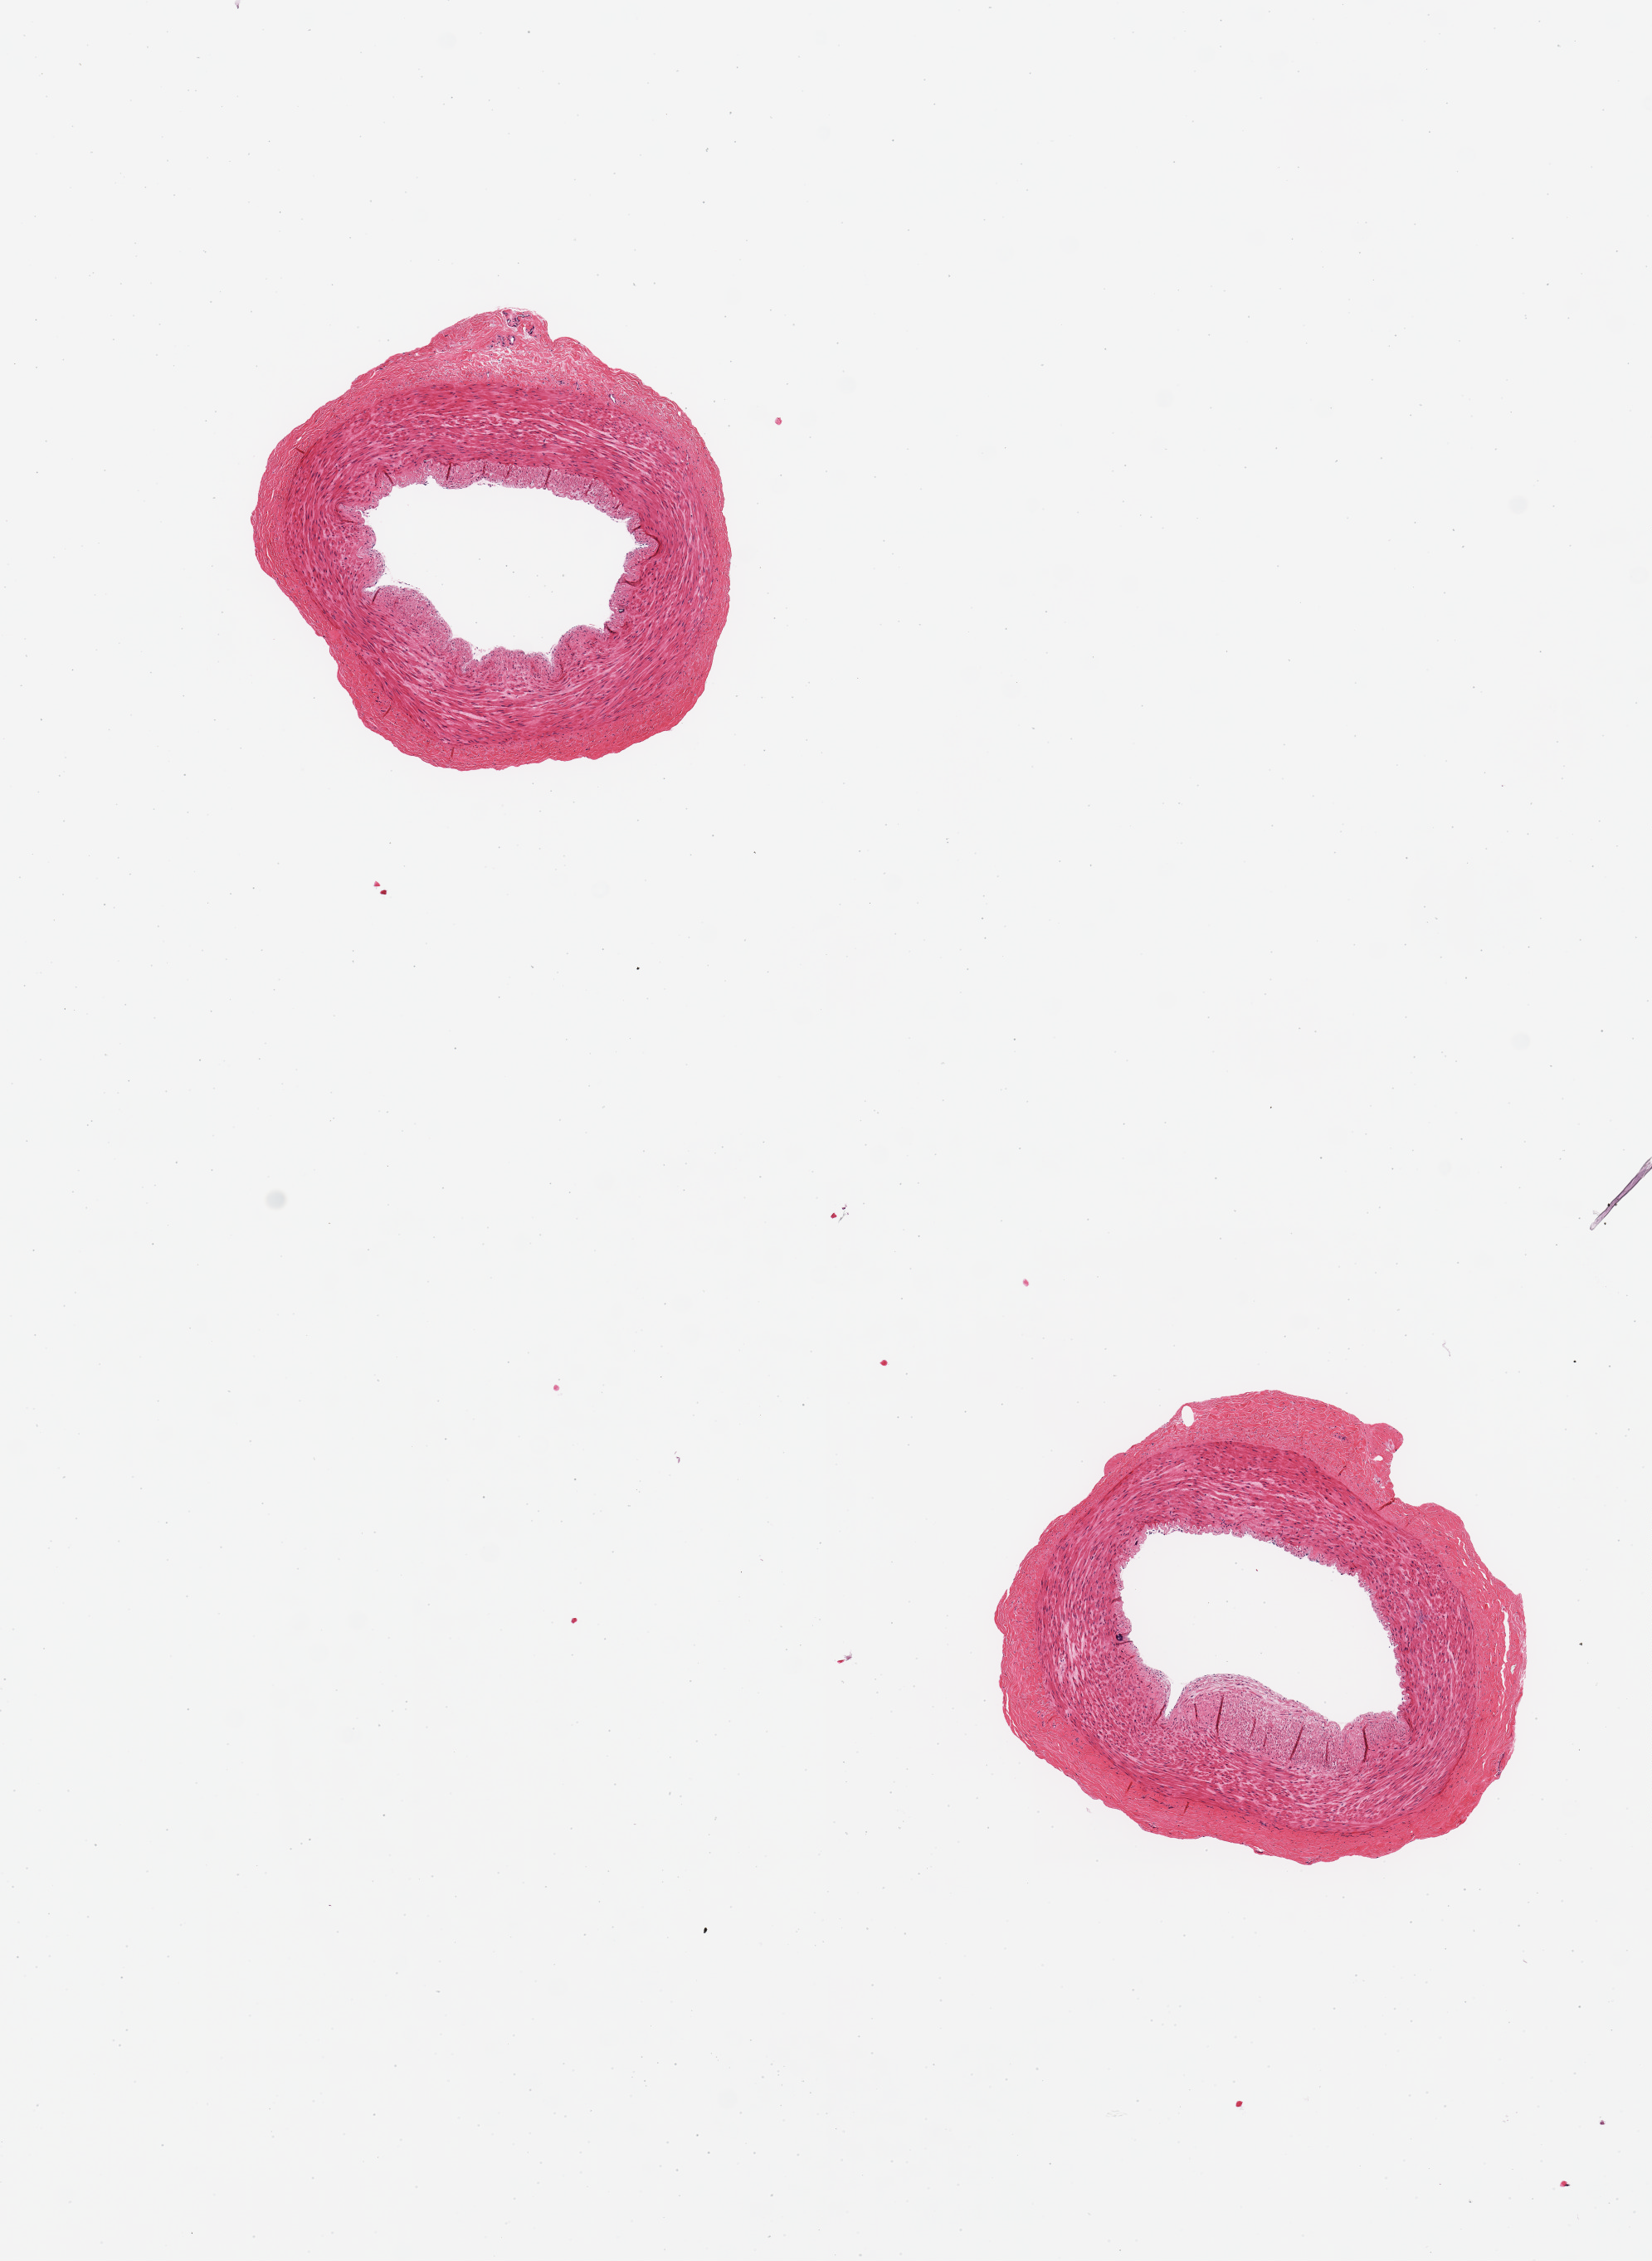
Digitized H&E-stained section — shown as a low-resolution overview of the whole scanned area (about 7.9 x 10.8 mm); PAXgene-fixed paraffin-embedded (PFPE) section; section of tibial artery (target tissue); donor tissue sample. Donor sex: male.
* pathologist's review note for this sample: 2 pieces, trace adherent fibrous tissue; no atherosis